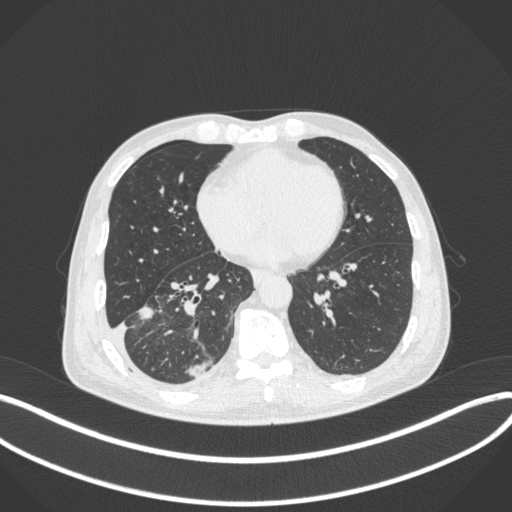
Chest CT, one axial slice; reconstruction kernel B31f; 120 kVp; lung window (W 1500 / L -600 HU); 512 × 512 image matrix, field of view 400 × 400 mm. Male patient, age 64 years. From the clinical record (not read from this slice): clinical TNM (as recorded): T3 N0 M0; histopathological grade: G2-3.
Structures marked on this image (rectangle marked by the reading radiologist):
- lung tumour (recorded histology: adenocarcinoma): bounding box [x1, y1, x2, y2] px = [131, 303, 156, 323]